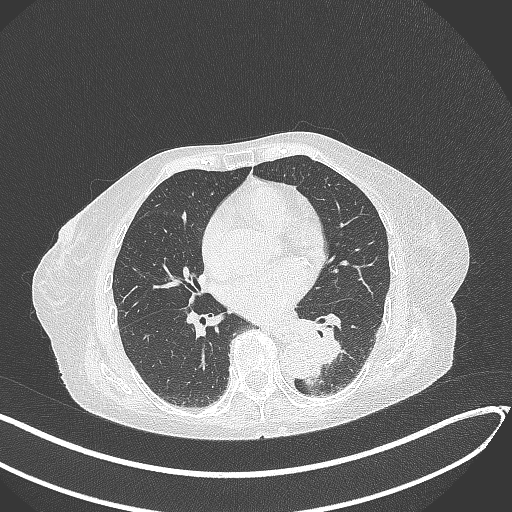
Chest CT, one axial slice. Position 114 of 324 along the scan axis. Reconstruction kernel B70f. 120 kVp. Lung window (W 1500 / L -600 HU). 512 × 512 image matrix, field of view 400 × 400 mm. Female patient, age 82 years. Case-level facts recorded for this patient, not image findings: clinical TNM (as recorded): T1b N0 M1.
Structures marked on this image (rectangle marked by the reading radiologist):
- lung tumour (recorded histology: adenocarcinoma): bounding box <294,317,350,369> (left, top, right, bottom; pixels)